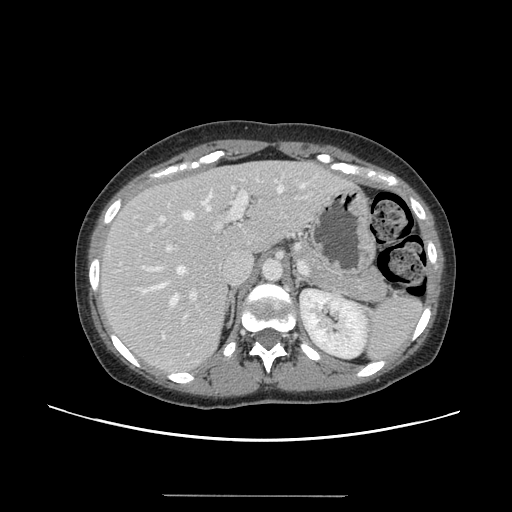
Contrast-enhanced abdominal CT, one axial slice; position 95 of 144 along the scan axis; 120 kVp; intravenous contrast given; soft-tissue window (W 400 / L 40 HU); 2.5 mm slice thickness; 512 × 512 image matrix, field of view 380 × 380 mm. Female patient, age 53 years. From the clinical record (not read from this slice): diagnosis: colorectal cancer liver metastases, imaged before liver resection; multiple liver metastases: yes; largest metastasis: 1.1 cm; disease in both lobes: no.
Annotated regions visible in this slice (manually delineated by an expert):
- hepatic veins: bounding box <143,184,305,305> (left, top, right, bottom; pixels)
- liver: <98,162,343,374>
- planned liver remnant (the part of the liver to remain after resection): <98,162,309,300>
- portal vein (with intrahepatic branches): <146,179,308,318>